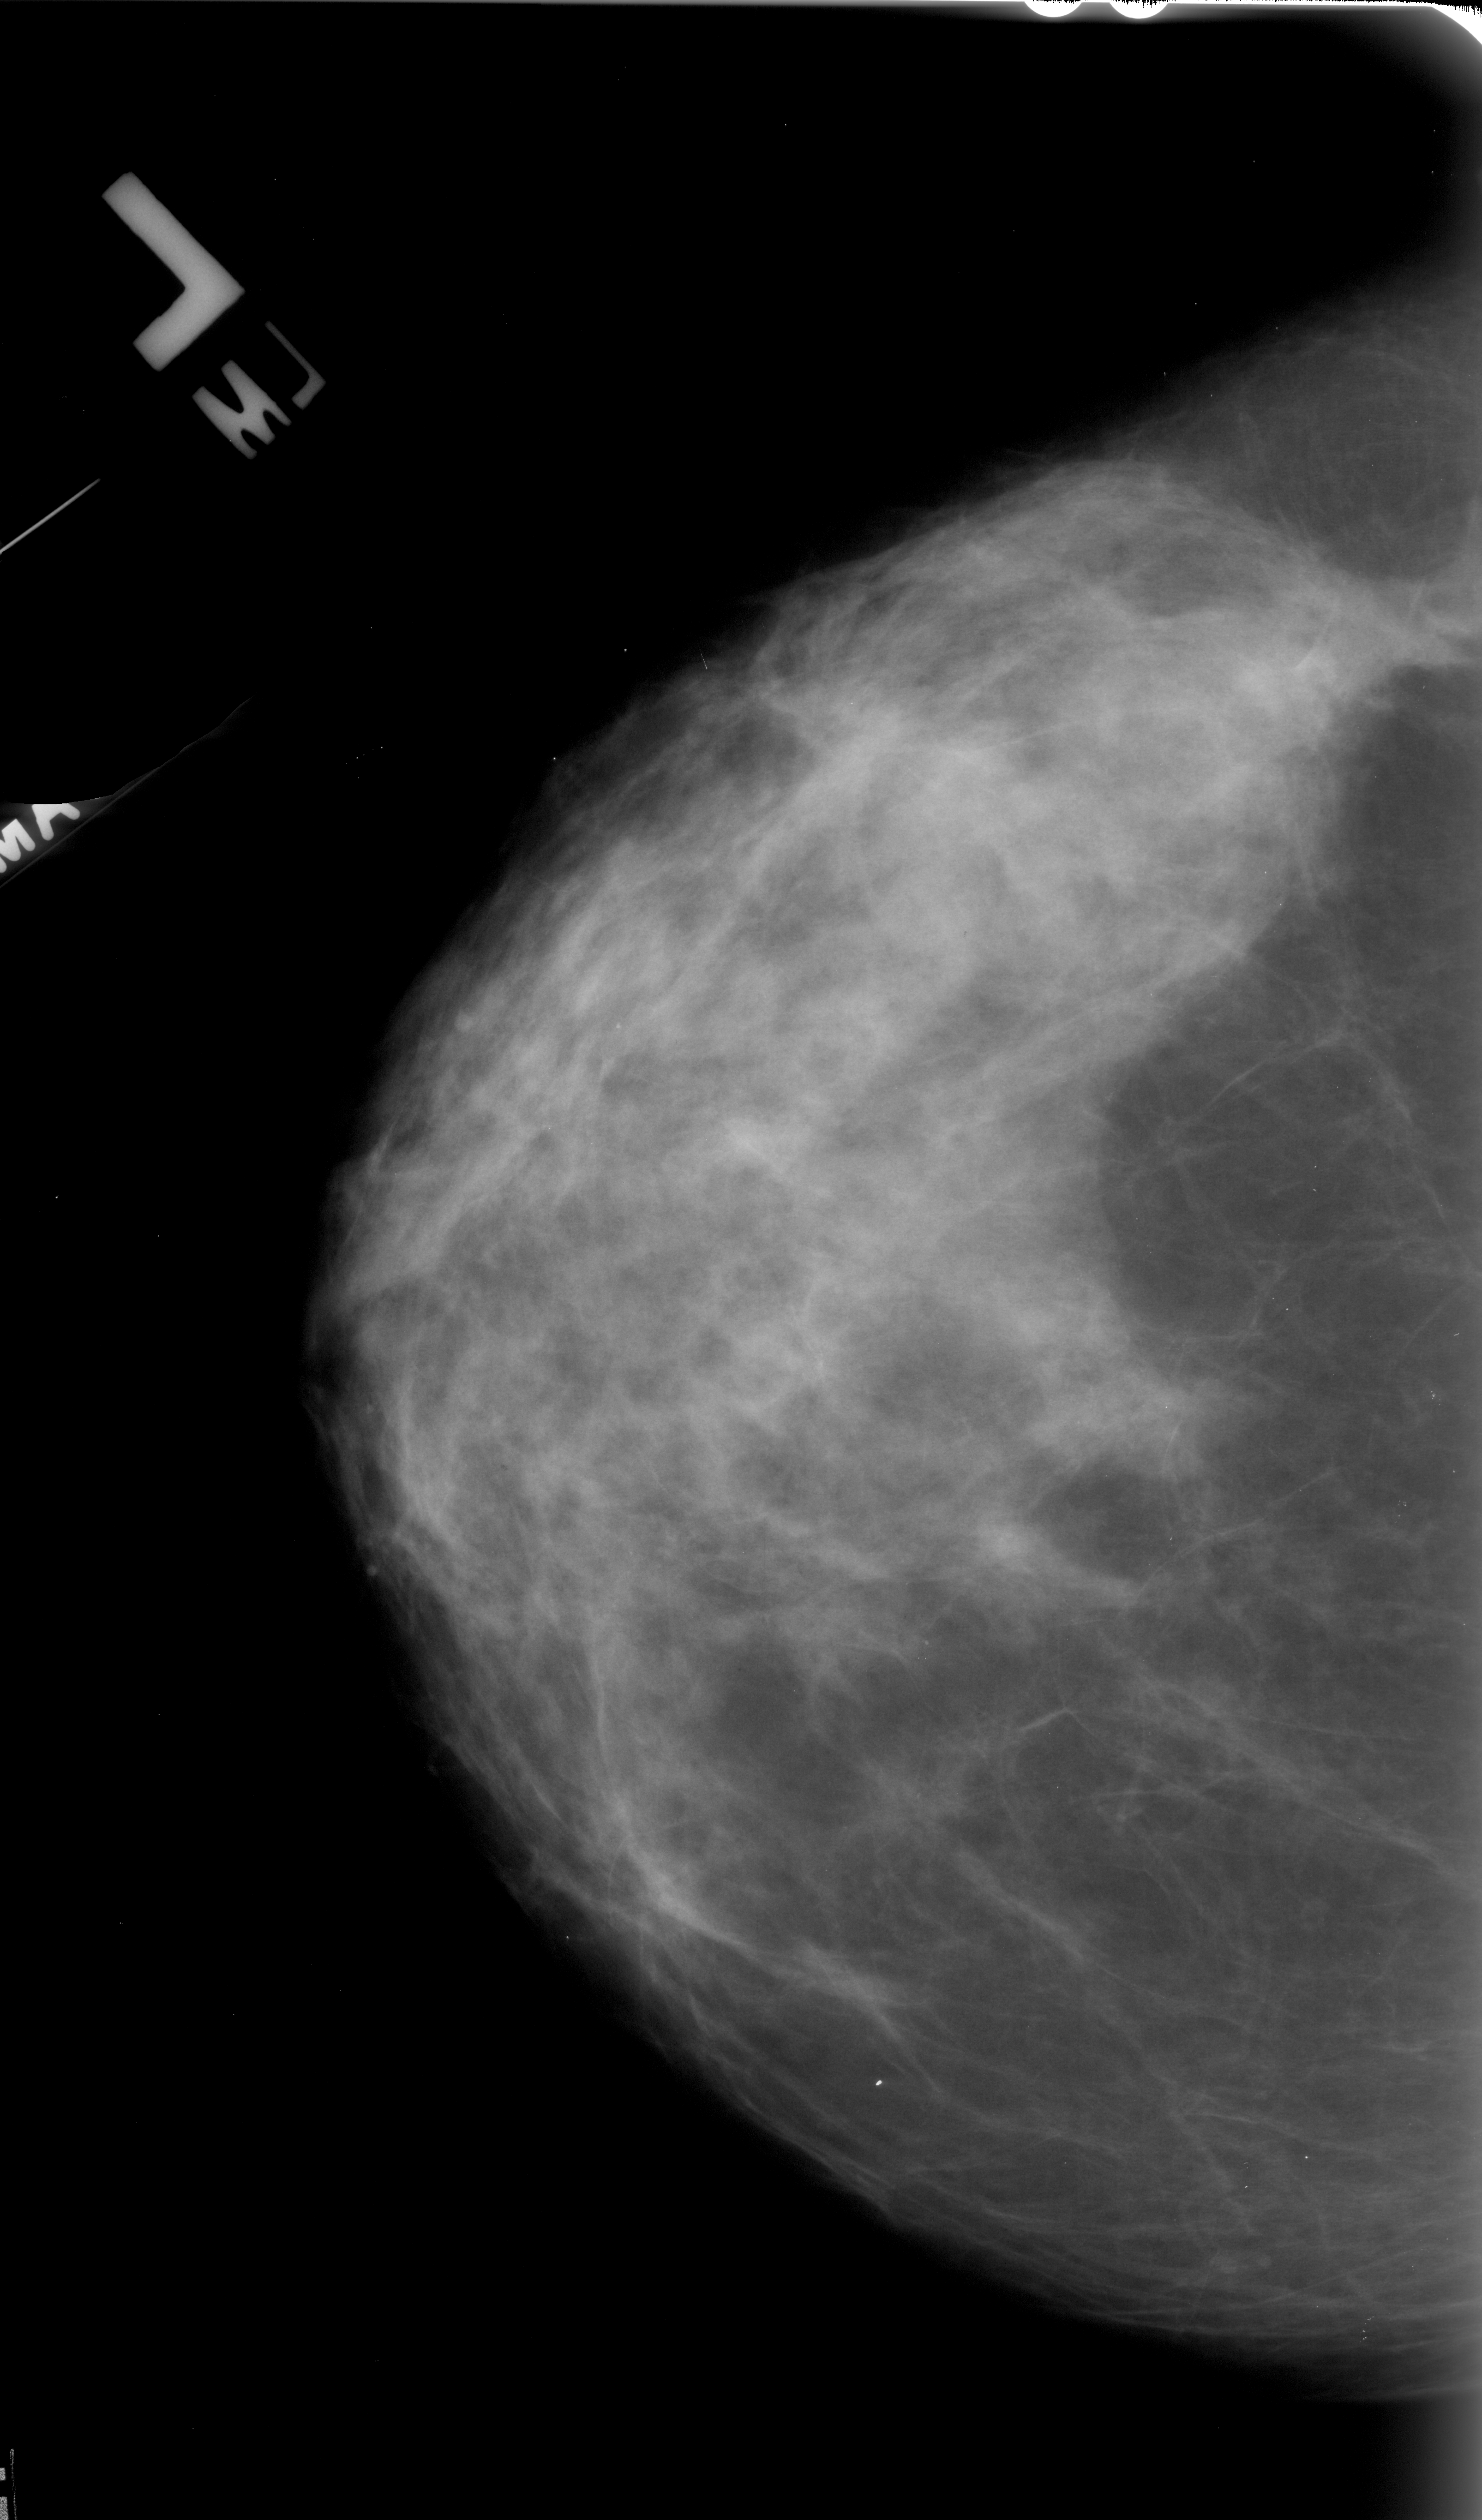
Scanned film-screen mammogram; left breast; craniocaudal (CC) view; BI-RADS breast density category 3 (scale 1–4).
- Marked abnormality: mass, shape architectural distortion, margins spiculated; BI-RADS assessment category 5; pathology result (as recorded, not read from the image): malignant.